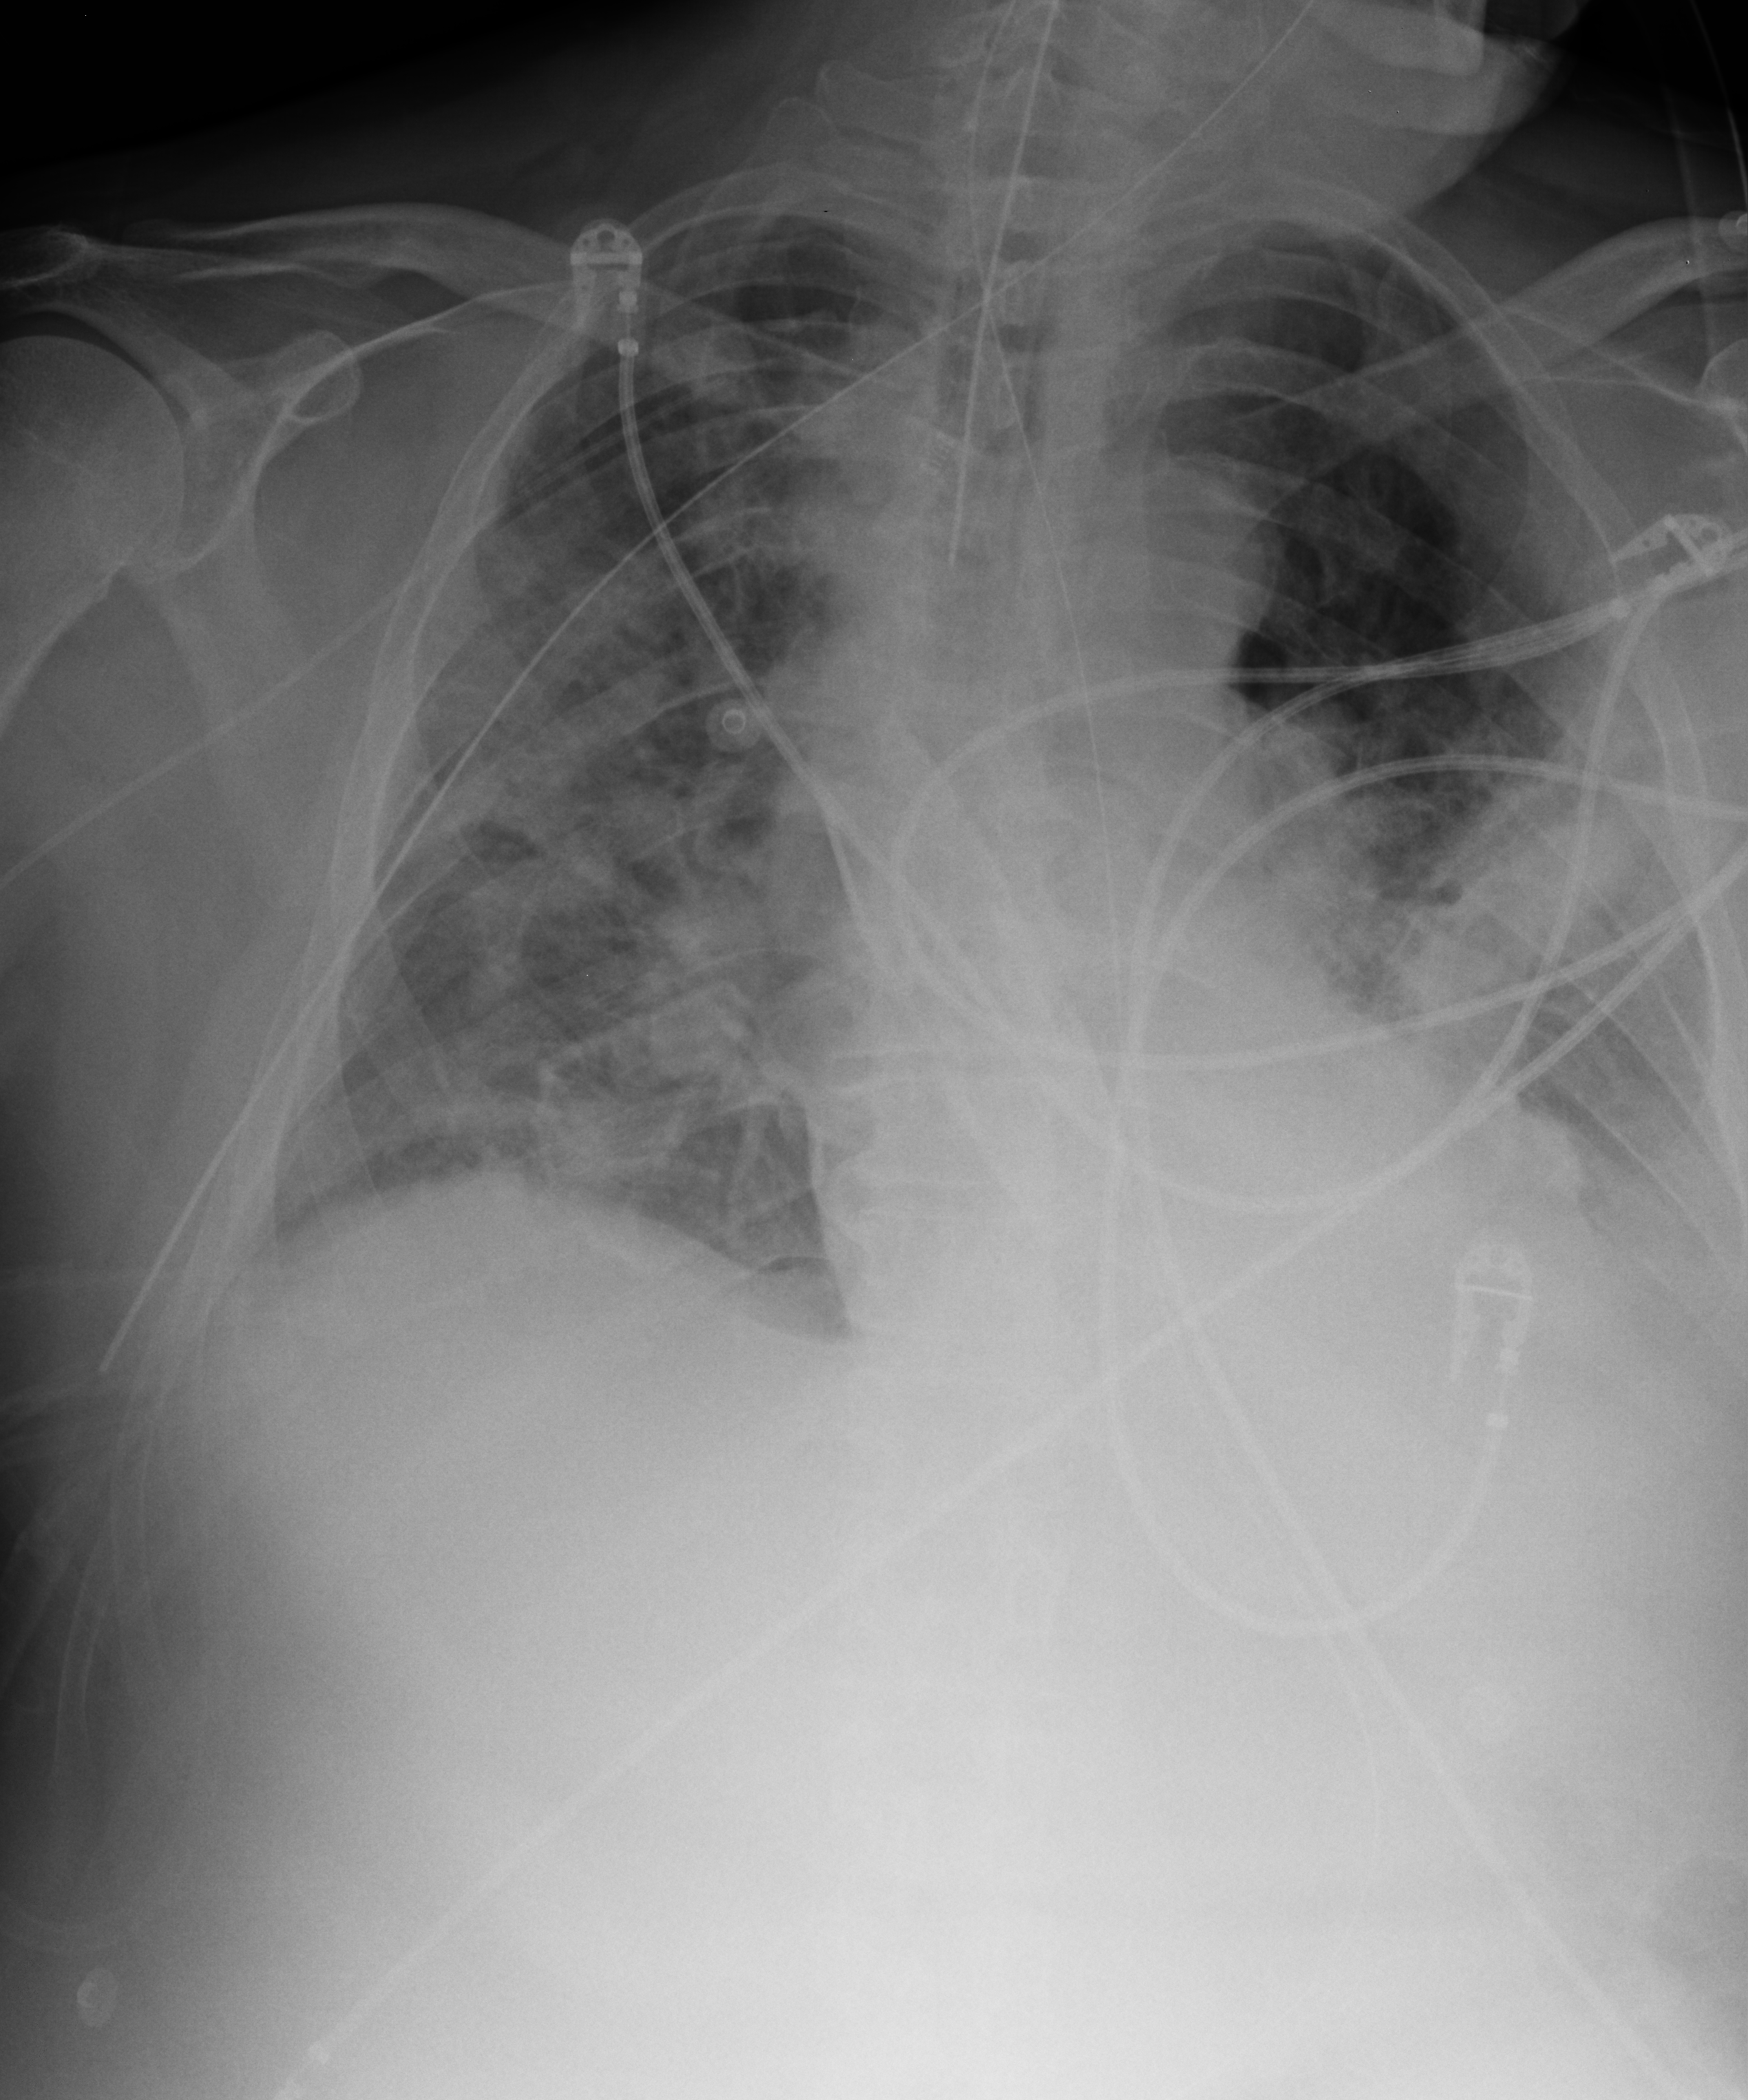
Portable chest radiograph, anteroposterior (AP) projection. Male patient hospitalised with COVID-19, age 60–74 years.
Admission-level facts for this patient (not findings on this image; timing relative to this image not recorded): length of hospital stay: 24 days; mechanically ventilated during this hospital stay: yes; admitted to intensive care during this hospital stay: yes.